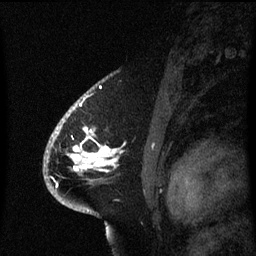
Breast MRI (dynamic contrast-enhanced), one sagittal slice. Position 44 of 60 along the scan axis. Dynamic contrast-enhanced series, image 2 of 3 at this slice position (ordered by acquisition). 1.5 T. TE 4.2 ms, TR 8.4 ms. 256 × 256 image matrix. Female patient, age 53 years. Case-level facts recorded for this patient, not image findings: setting: breast cancer imaged before/during neoadjuvant chemotherapy; receptor status: HR-positive, HER2-negative.
Outlined on this slice (semi-automatic segmentation, software-assisted and operator-edited):
- analysis volume of interest (the breast-tissue region the enhancement analysis was run in; not a lesion): bounding box [x1, y1, x2, y2] px = [49, 108, 124, 201]
- tumour enhancement mask (voxels above the 70 % enhancement threshold inside the analysis volume of interest): [58, 114, 117, 171]